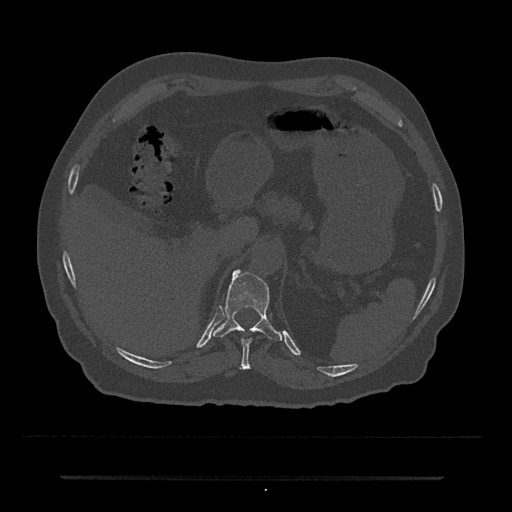
CT including the spine, one axial slice; position 191 of 797 along the scan axis; 120 kVp; bone window (W 1800 / L 400 HU); 512 × 512 image matrix. Male patient, age 69 years. From the clinical record (not read from this slice): primary cancer: prostate.
Structures marked on this image (semi-automatic segmentation, software-assisted and operator-edited):
- T10 vertebra: bounding box <241,338,252,369> (left, top, right, bottom; pixels)
- T11 vertebra: <213,269,283,341>